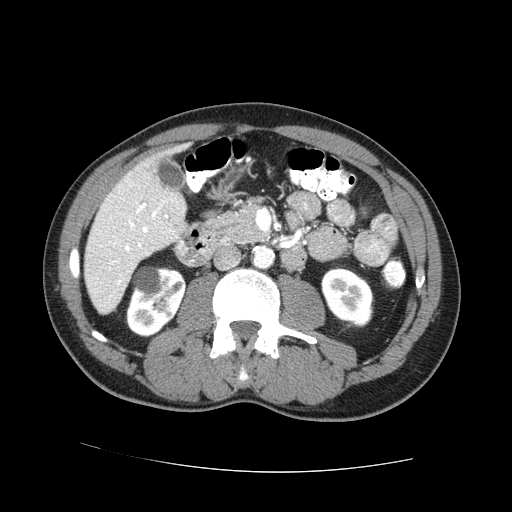
Contrast-enhanced abdominal CT (liver protocol), one axial slice. Slice 21 of 73 in the series (ordered by position). Reconstruction kernel STANDARD. 100 kVp. One of 2 acquisitions stored at this slice position. Soft-tissue window (W 400 / L 40 HU). 2.5 mm slice thickness. 512 × 512 image matrix, field of view 380 × 380 mm. Case-level facts recorded for this patient, not image findings: diagnosis: hepatocellular carcinoma (patient treated with transarterial chemoembolisation; whether this scan precedes or follows treatment is not stated here); TNM stage (as recorded): Stage-IVA; Child-Pugh class: A.
Structures marked on this image (semi-automatic segmentation, software-assisted and operator-edited):
- liver parenchyma outside the tumour (the mass and vessels are separate outlines, so this box may not span the whole liver): bounding box <84,142,190,314> (left, top, right, bottom; pixels)
- liver vessels: <113,203,168,284>